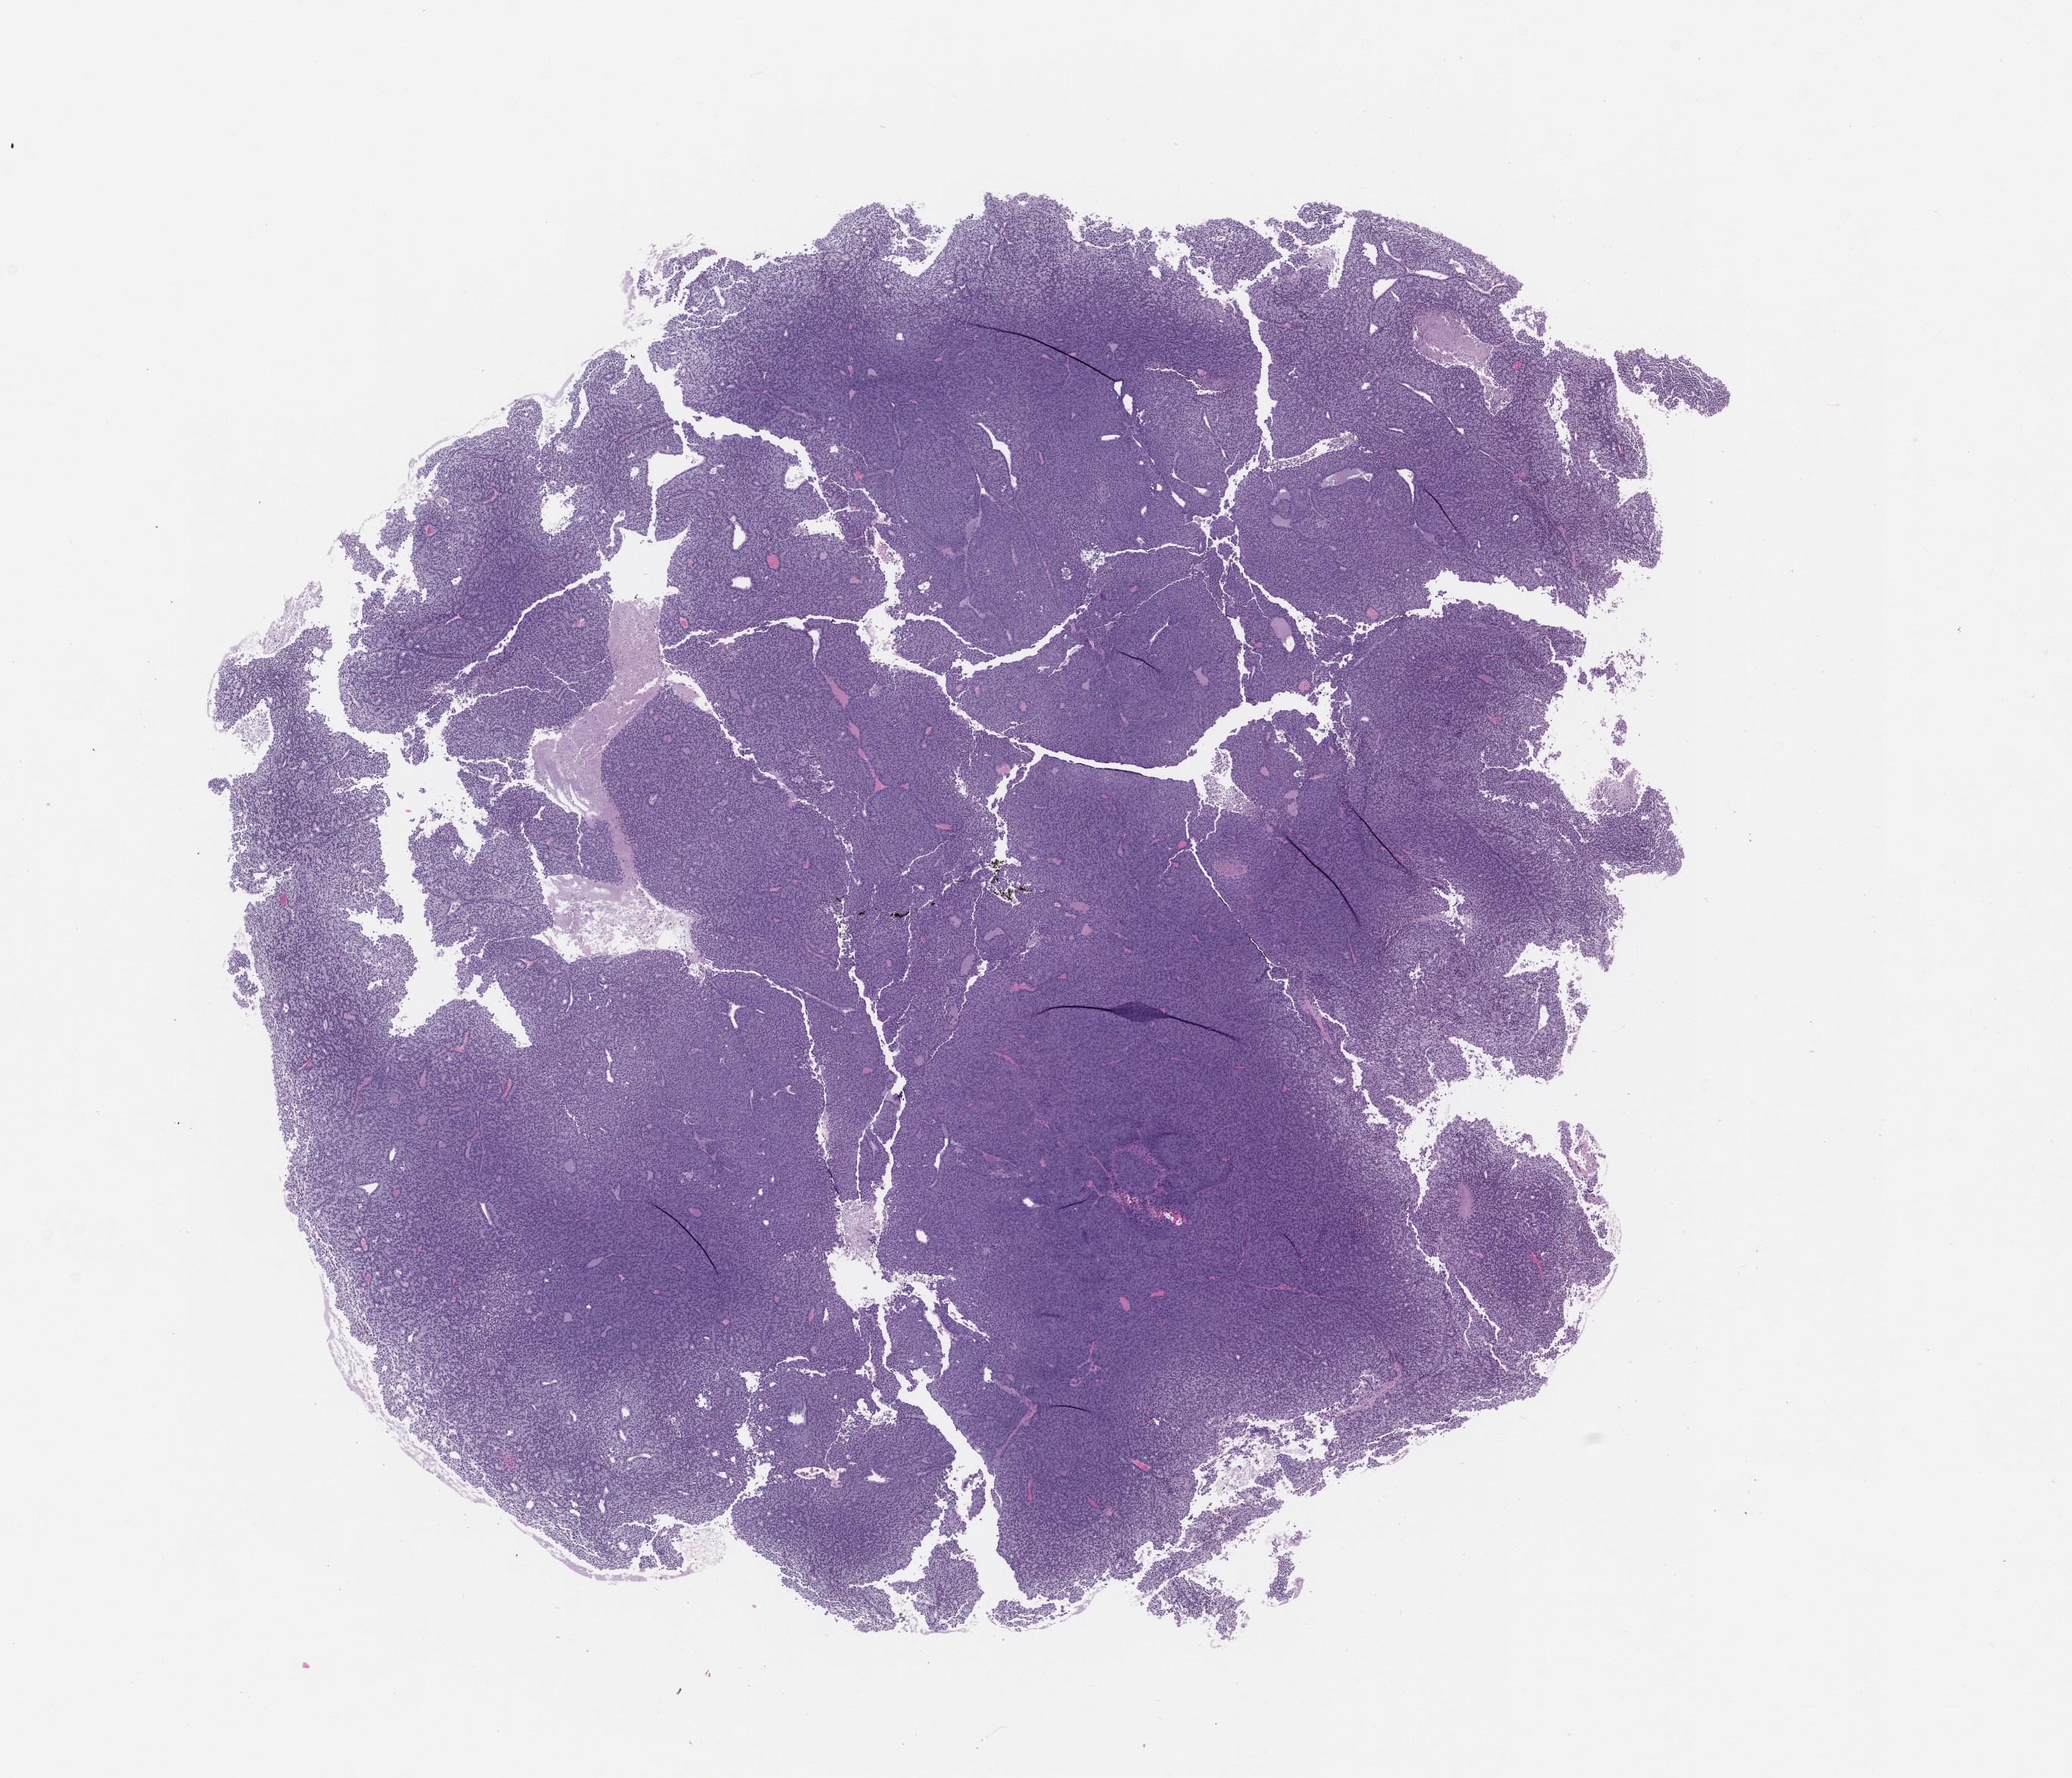
Whole-slide image, hematoxylin and eosin (H&E): patient-derived xenograft (human tumor grown in a mouse), passage 1, a low-resolution overview of the entire scanned area, about 11.0 x 9.5 mm, FFPE section, tumor site category: head and neck.
• originating patient diagnosis: Acinar Cell Carcinoma